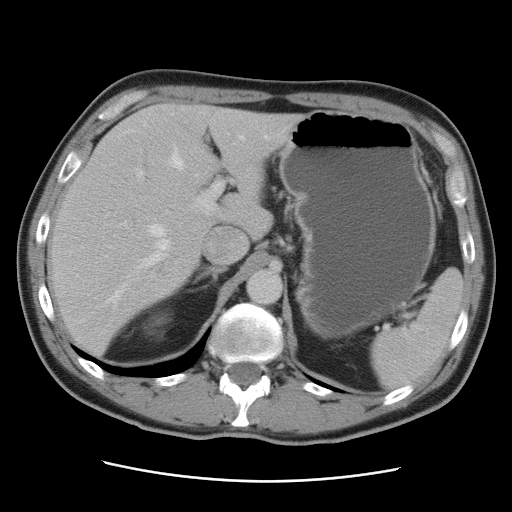
Contrast-enhanced abdominal CT, one axial slice; position 60 of 89 along the scan axis; 120 kVp; intravenous contrast given; soft-tissue window (W 400 / L 40 HU); 512 × 512 image matrix, field of view 366 × 366 mm. Male patient, age 59 years. From the clinical record (not read from this slice): diagnosis: colorectal cancer liver metastases, imaged before liver resection; multiple liver metastases: yes; largest metastasis: 0.6 cm; chemotherapy before resection: no.
Outlined on this slice (outlined manually by an expert reader):
- hepatic veins: bounding box <105,135,269,305> (left, top, right, bottom; pixels)
- liver: <50,104,303,356>
- planned liver remnant (the part of the liver to remain after resection): <85,104,273,241>
- portal vein (with intrahepatic branches): <120,169,224,226>